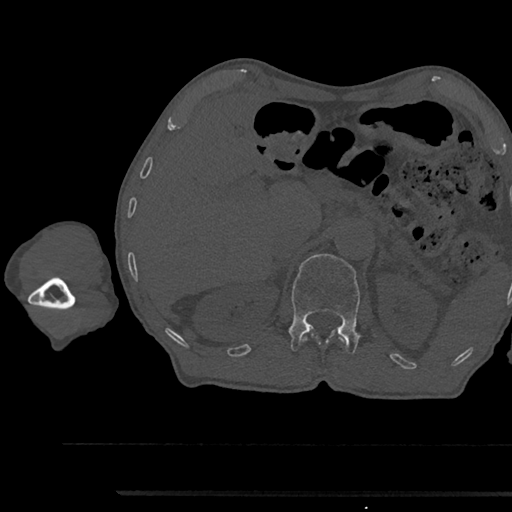
CT including the spine, one axial slice; slice 665 of 797 in the series (ordered by position); 120 kVp; bone window (W 1800 / L 400 HU); 0.5 mm slice thickness; 512 × 512 image matrix, field of view 367 × 367 mm. Patient: male, 79 years. From the clinical record (not read from this slice): primary cancer: prostate.
Outlined on this slice (semi-automatic segmentation, software-assisted and operator-edited):
- L1 vertebra: bounding box [x1, y1, x2, y2] px = [288, 254, 362, 354]
- T12 vertebra: [305, 335, 332, 342]